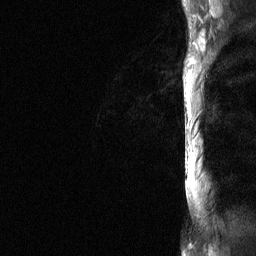
Breast MRI (dynamic contrast-enhanced), one sagittal slice; slice 52 of 64 in the series (ordered by position); dynamic contrast-enhanced study with each time point stored as its own series, time point 2 of 3 at this slice position (early post-contrast, ordered by acquisition time); 1.5 T; TE 4.8 ms, TR 27 ms; 256 × 256 image matrix. Female patient, age 36 years. From the clinical record (not read from this slice): setting: breast cancer imaged before/during neoadjuvant chemotherapy; receptor status: HR-positive, HER2-negative.
Structures marked on this image (semi-automatic segmentation, software-assisted and operator-edited):
- analysis volume of interest (the breast-tissue region the enhancement analysis was run in; not a lesion): bounding box (x1, y1, x2, y2) in pixels: (183, 68, 187, 199)
- tumour enhancement mask (voxels above the 90 % enhancement threshold inside the analysis volume of interest): (185, 85, 187, 93)